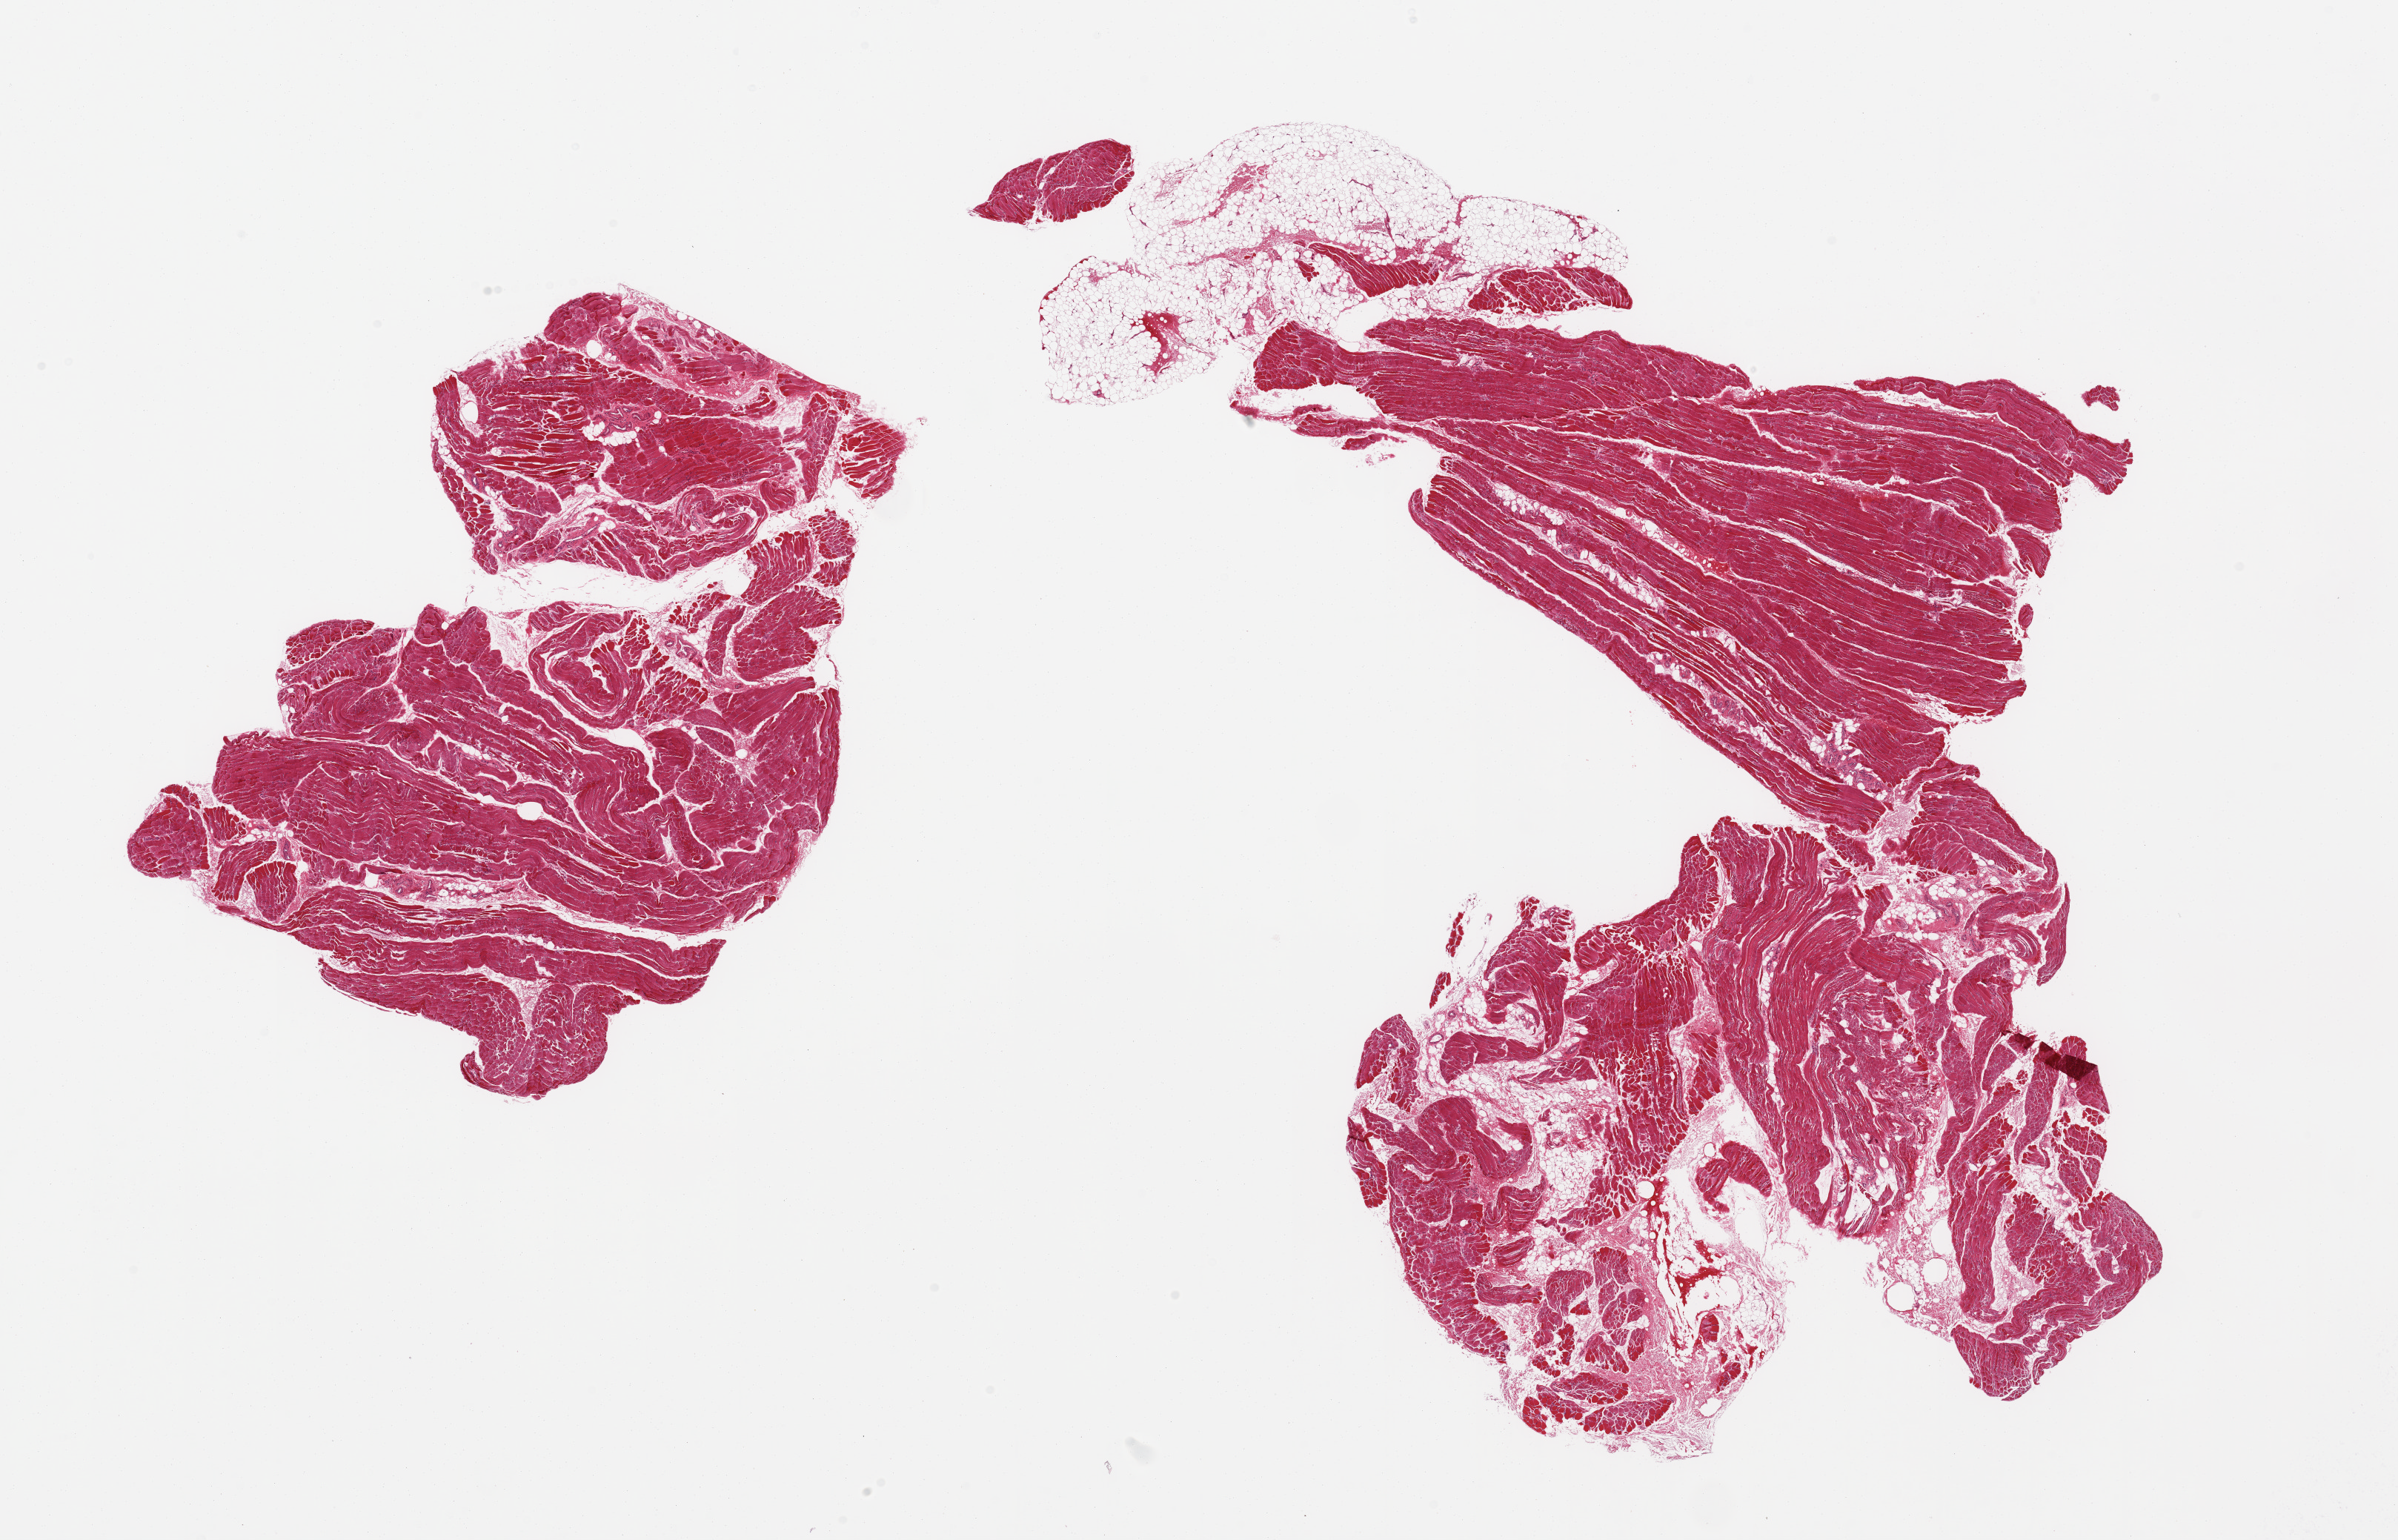
H&E whole-slide image, low-resolution overview of the scanned area, about 25.6 x 16.4 mm; PAXgene-fixed paraffin-embedded (PFPE) section; sampled site (target tissue): skeletal muscle; donor tissue sample. Male donor.
Pathologist's review note for this sample: 2 pieces; one consists of 10% external and 10% internal fat and other less than 10% internal fat.